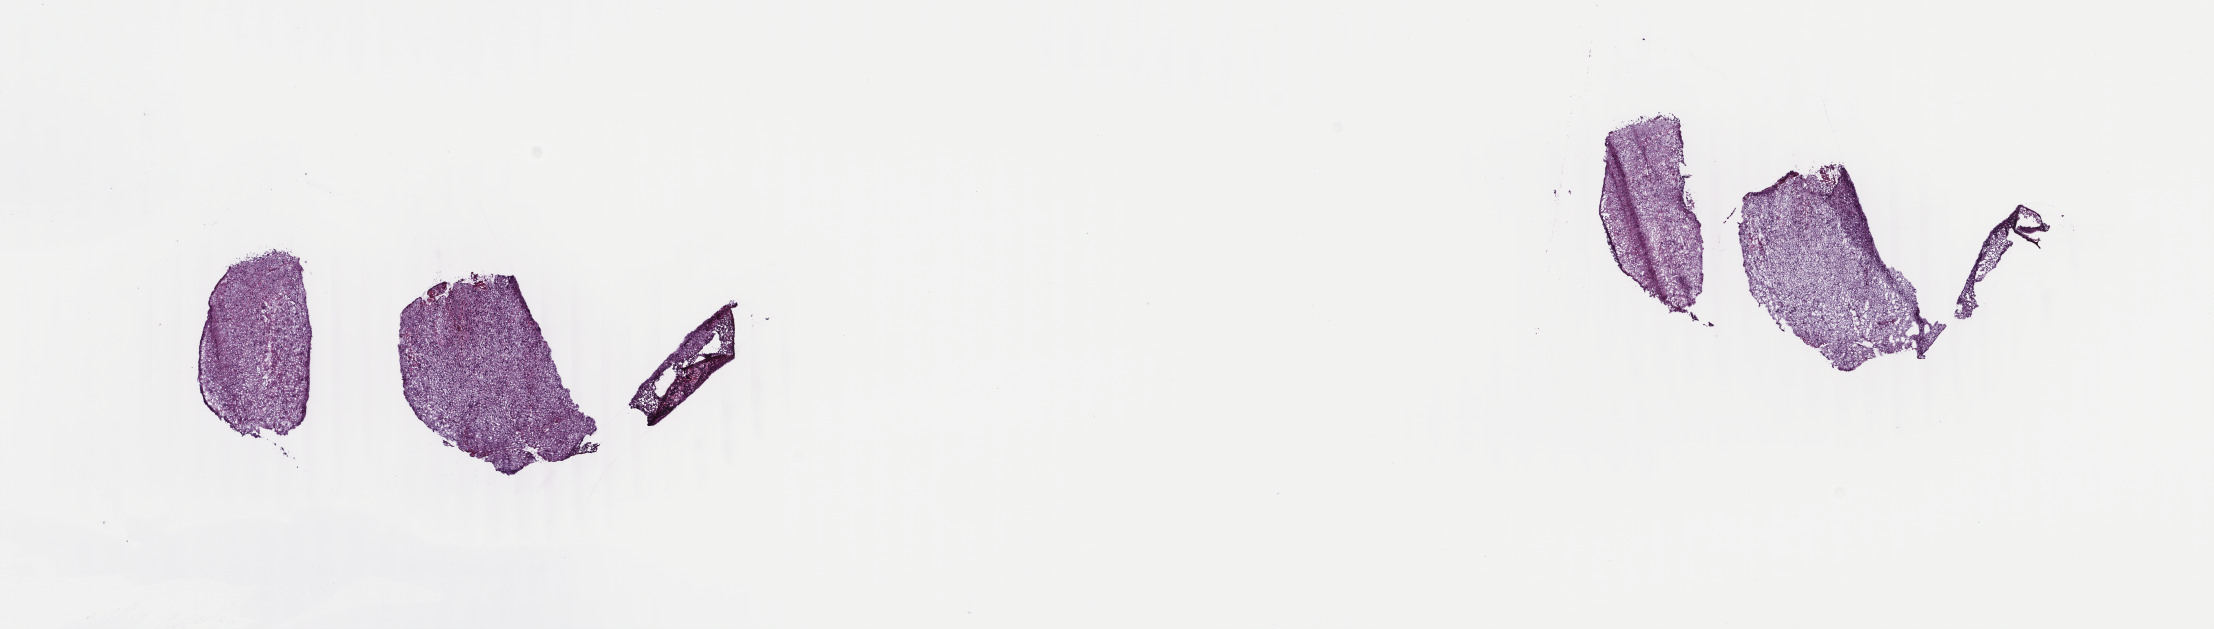
Digitized Hematoxylin and eosin (H&E) stained tissue section (whole slide) — whole scanned area (about 17.6 x 5.0 mm) shown as a low-resolution overview, frozen section from the top of the tissue portion, primary tumour sample from the brain. Male patient; age at initial diagnosis 54 years. Histologic grade: G2 (moderately differentiated). Slide review estimates, as recorded: tumour cells 30%, tumour nuclei 75%, normal cells 10%, stromal cells 60%, necrosis 0%. Infiltration values recorded for this section: lymphocyte infiltration 0%, monocyte infiltration 0%, neutrophil infiltration 0%.
* histologic diagnosis: Oligodendroglioma, NOS (cerebrum)